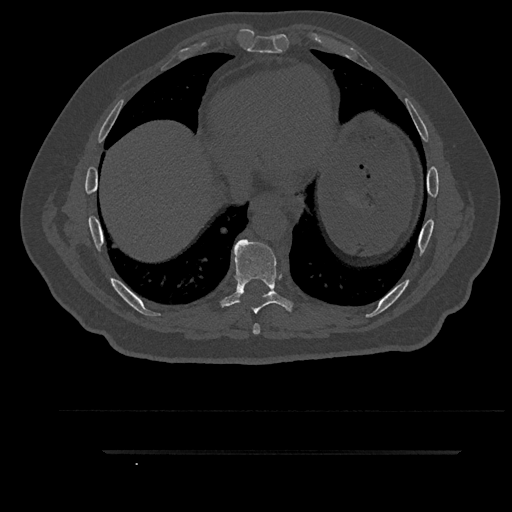
CT including the spine, one axial slice; slice 478 of 797 in the series (ordered by position); reconstruction kernel Br40s/3; 120 kVp; bone window (W 1800 / L 400 HU); 0.5 mm slice thickness; 512 × 512 image matrix, field of view 432 × 432 mm. Male patient, age 63 years. From the clinical record (not read from this slice): primary cancer: renal; vertebrae with lytic lesions (as recorded): T8.
Annotated regions visible in this slice (semi-automatically segmented with operator editing):
- T7 vertebra: box from (x=253, y=324) to (x=260, y=335) px
- T8 vertebra: (x=216, y=239)–(x=296, y=314)